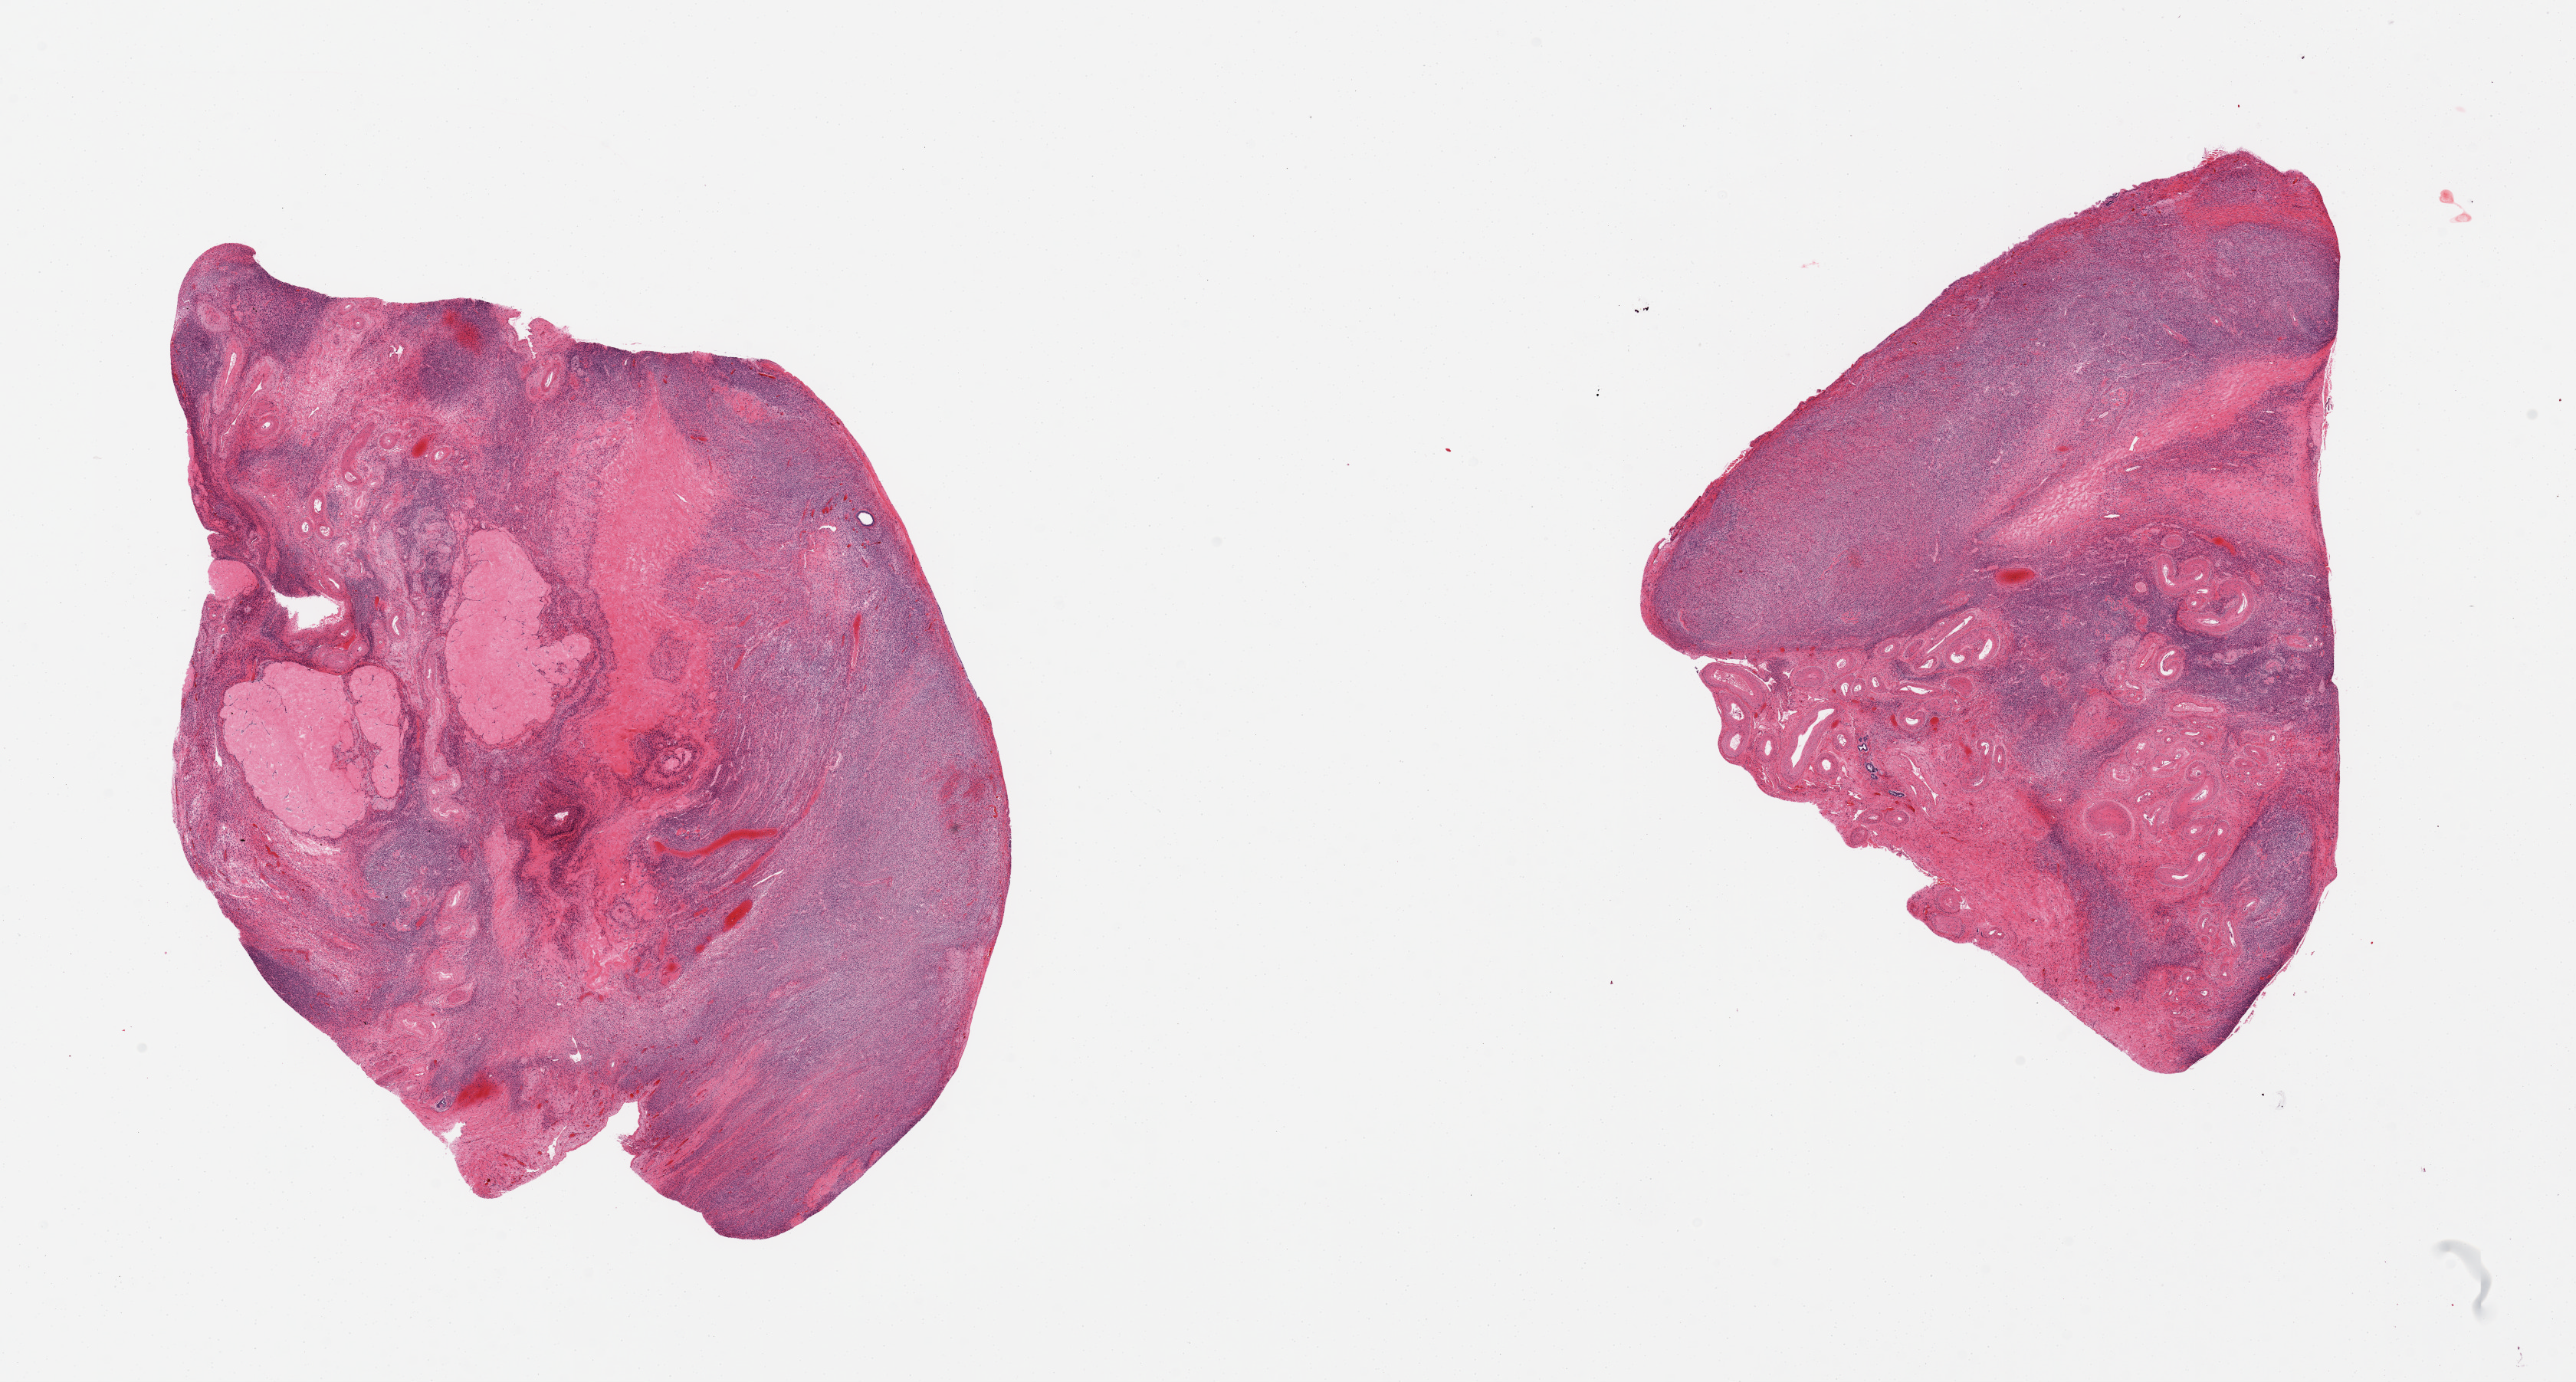
Whole-slide image, H&E stain, brightfield, shown as a low-resolution overview of the whole scanned area (about 26.6 x 14.3 mm, from a 20x scan). PAXgene-fixed, paraffin-embedded tissue. Section of ovary (target tissue). Tissue donor sample.
- reviewer comment on this tissue sample: 2 pieces, post-menopausal ovarian parenchyma; no uterine tissue present